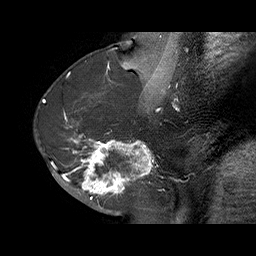
Breast MRI (dynamic contrast-enhanced), one sagittal slice. Position 31 of 70 along the scan axis. Dynamic contrast-enhanced series, time point 2 of 6 at this slice position (early post-contrast). 1.5 T. TE 4.5 ms, TR 32.4 ms. 3 mm slice thickness. 256 × 256 image matrix, field of view 180 × 180 mm. Female patient. From the clinical record (not read from this slice): setting: breast cancer imaged before/during neoadjuvant chemotherapy; receptor status: HR-positive, HER2-negative.
Structures marked on this image (semi-automatic segmentation, software-assisted and operator-edited):
- analysis volume of interest (the breast-tissue region the enhancement analysis was run in; not a lesion): box from (x=71, y=128) to (x=159, y=202) px
- tumour enhancement mask (voxels above the 100 % enhancement threshold inside the analysis volume of interest): (x=71, y=133)–(x=153, y=200)